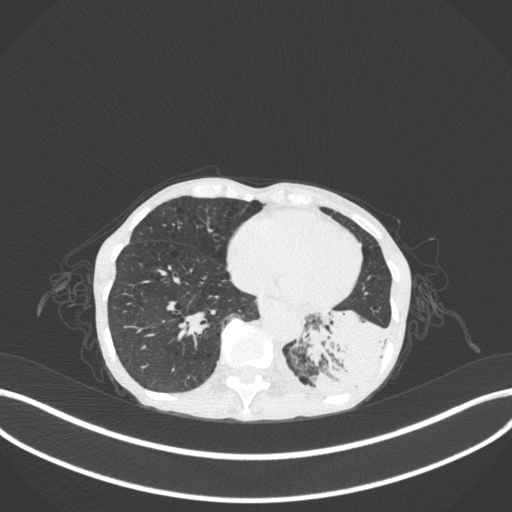
Chest CT, one axial slice. Position 67 of 347 along the scan axis. Reconstruction kernel B31f. 120 kVp. Lung window (W 1500 / L -600 HU). 1 mm slice thickness. 512 × 512 image matrix, field of view 400 × 400 mm. Patient: female, 70 years. From the clinical record (not read from this slice): clinical TNM (as recorded): T3 N0 M0; histopathological grade: G3.
Outlined on this slice (rectangle marked by the reading radiologist):
- lung tumour (recorded histology: small cell carcinoma): bounding box <295,297,394,404> (left, top, right, bottom; pixels)